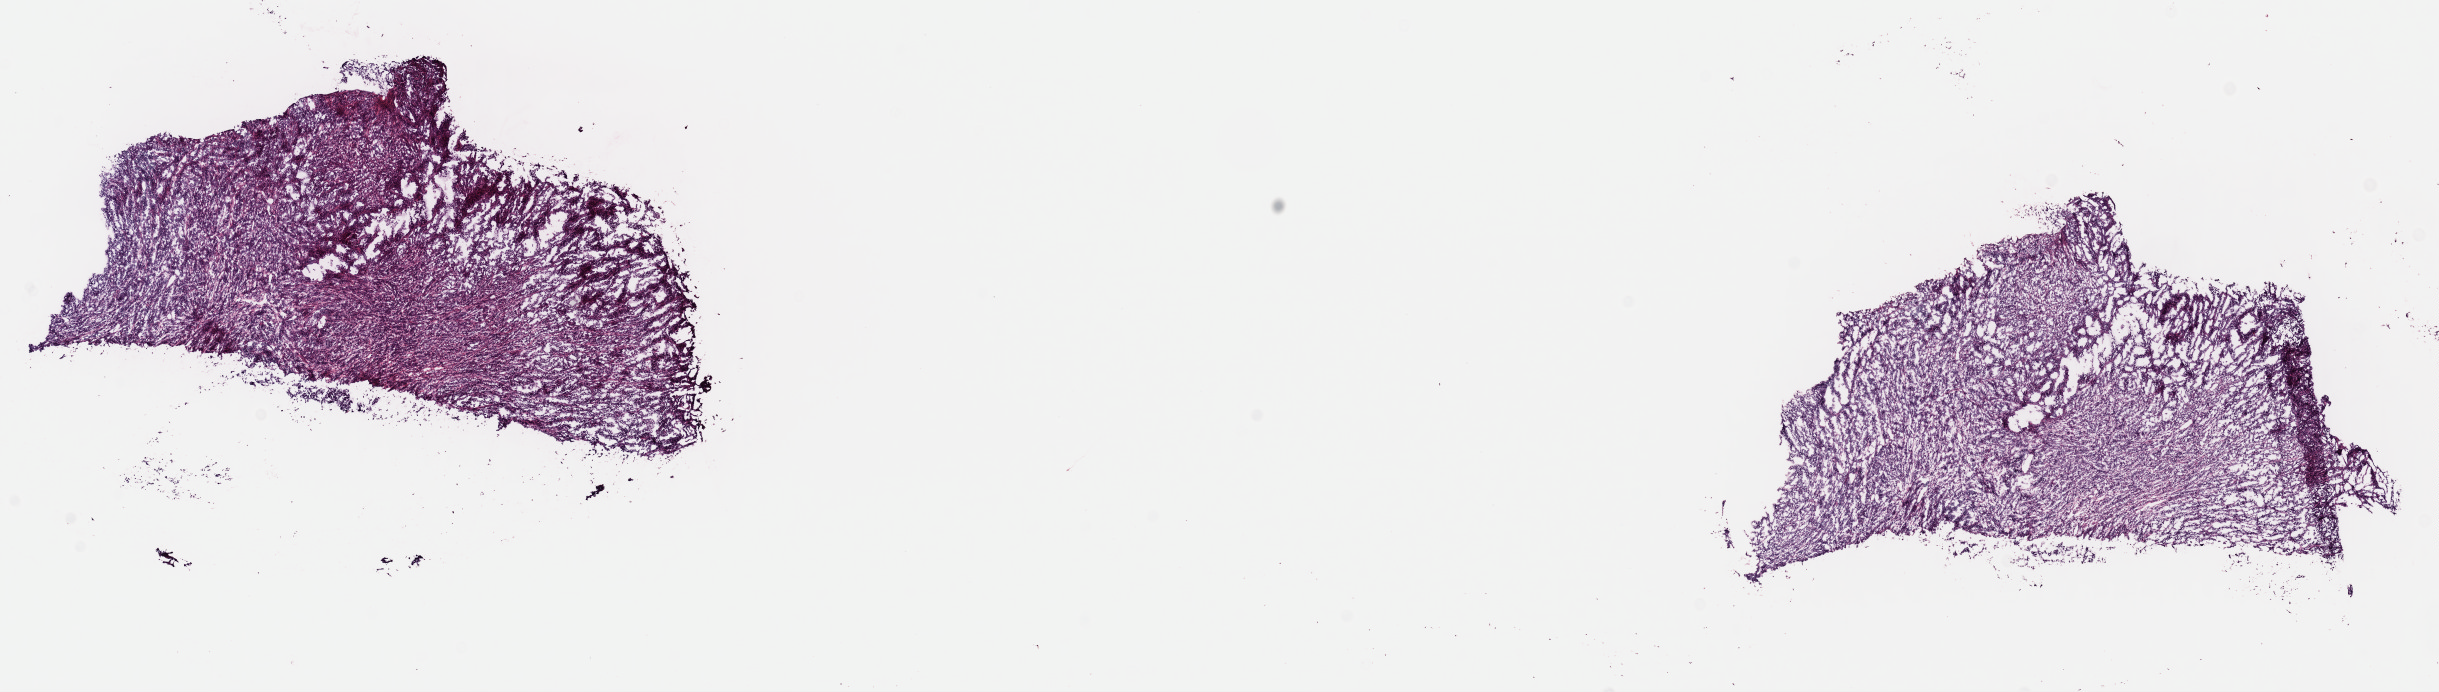
Digitized H&E tissue section (whole slide) — shown as a low-resolution overview of the whole scanned area (about 19.3 x 5.5 mm, slide scanned at 40x); frozen section from the top of the tissue portion; metastatic tumour sample, sampled site not recorded. Male patient; age at initial diagnosis 75 years. Slide review estimates, as recorded: tumour cells 85%, tumour nuclei 85%.
This section: metastatic tumour tissue. Patient diagnosis: Malignant melanoma, NOS.